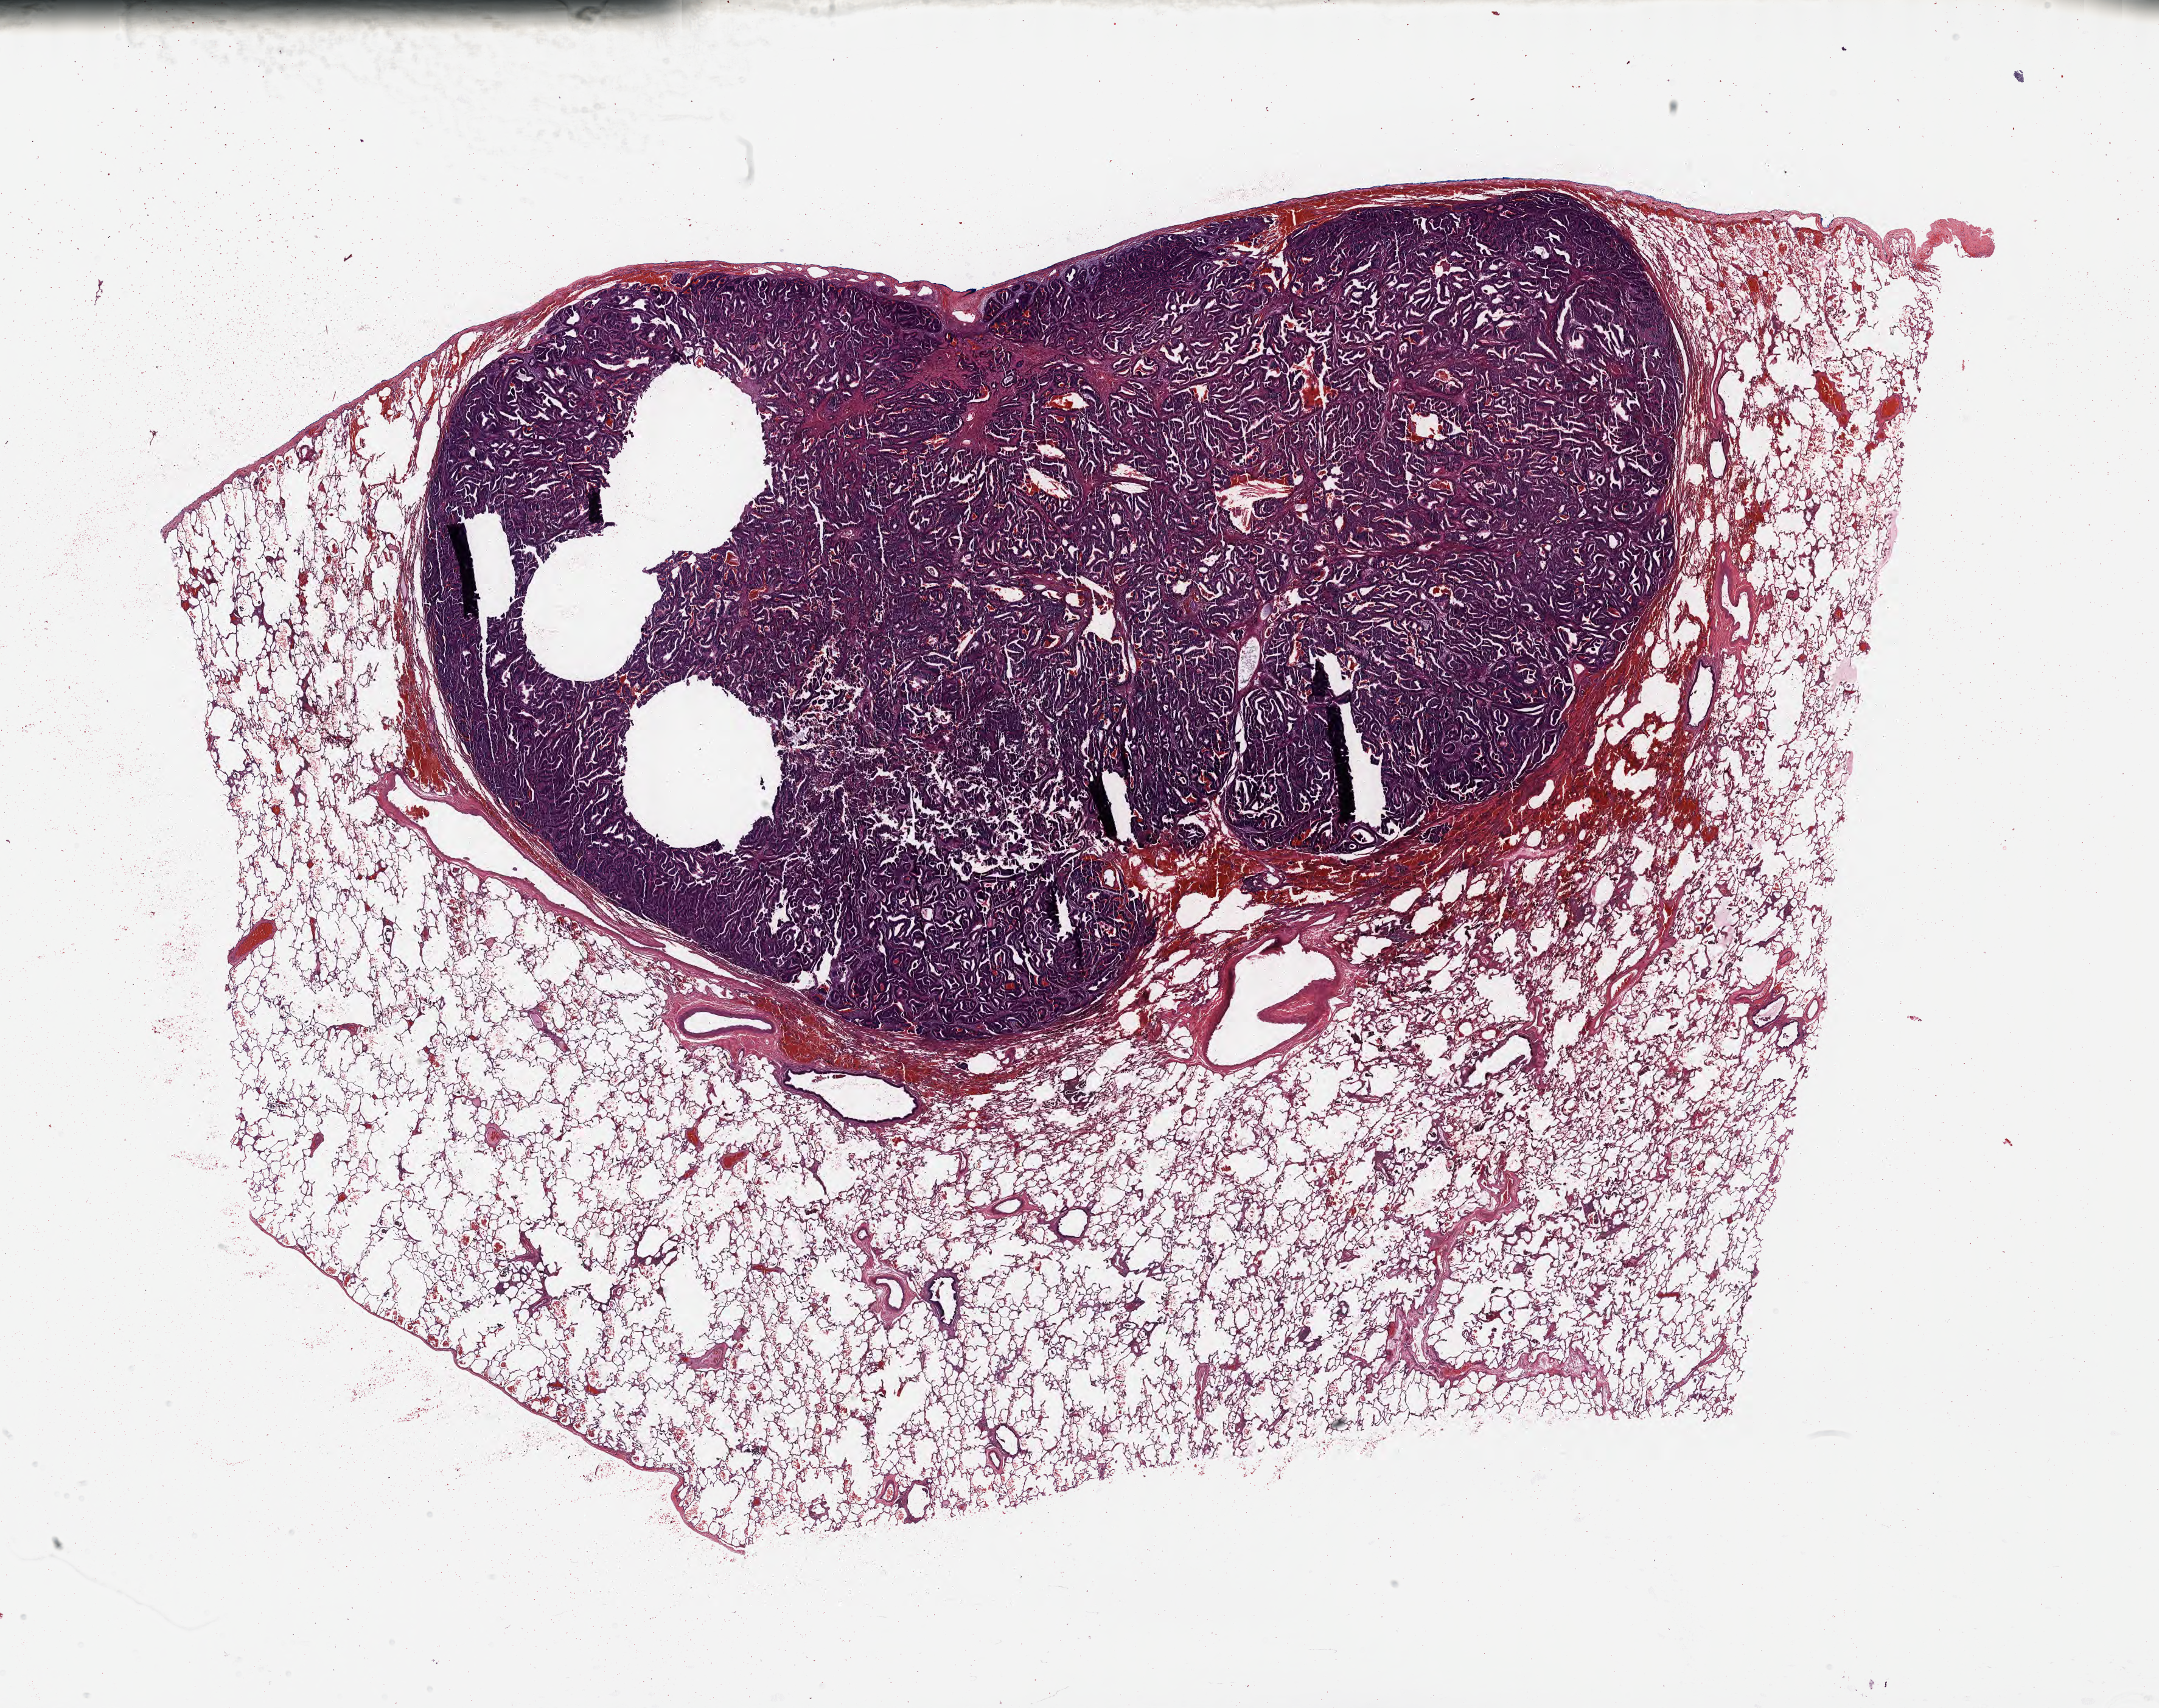
Whole-slide image, haematoxylin and eosin stain, whole scanned area (about 28.7 x 22.7 mm) shown as a low-resolution overview; tumor tissue; anatomic site: lung. Female patient.
Diagnosis: Adenocarcinoma, NOS.